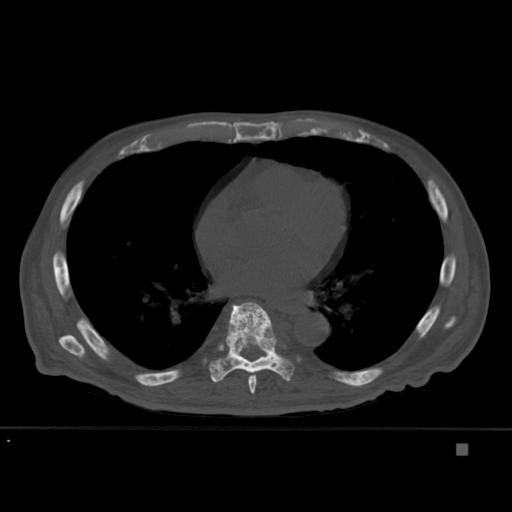
CT including the spine, one axial slice. Slice 266 of 451 in the series (ordered by position). Bone window (W 1800 / L 400 HU). 1.5 mm slice thickness. 512 × 512 image matrix. Male patient, age 75 years. Case-level facts recorded for this patient, not image findings: primary cancer: prostate.
Structures marked on this image (semi-automatic segmentation, software-assisted and operator-edited):
- T7 vertebra: bounding box (x1, y1, x2, y2) in pixels: (248, 317, 270, 394)
- T8 vertebra: (209, 302, 295, 383)
- T9 vertebra: (262, 356, 266, 357)